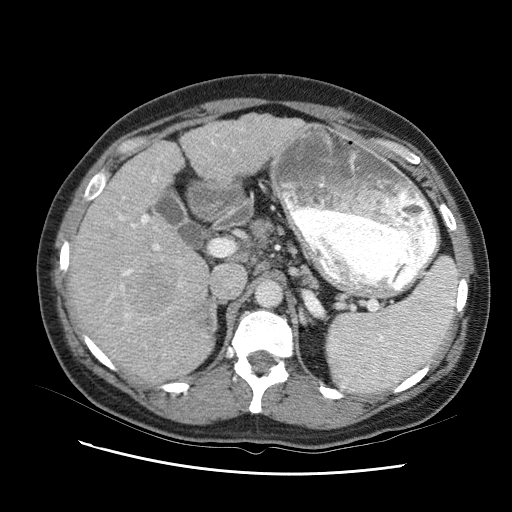
Contrast-enhanced abdominal CT (liver protocol), one axial slice. Slice 57 of 95 in the series (ordered by position). Reconstruction kernel STANDARD. 120 kVp. One of 2 acquisitions stored at this slice position. Soft-tissue window (W 400 / L 40 HU). 2.5 mm slice thickness. 512 × 512 image matrix, field of view 360 × 360 mm. From the clinical record (not read from this slice): diagnosis: hepatocellular carcinoma (patient treated with transarterial chemoembolisation; whether this scan precedes or follows treatment is not stated here); TNM stage (as recorded): Stage-I; Child-Pugh class: B; tumour differentiation: moderately differentiated; tumour nodularity: uninodular.
Outlined on this slice (semi-automatically segmented with operator editing):
- liver parenchyma outside the tumour (the mass and vessels are separate outlines, so this box may not span the whole liver): bounding box [x1, y1, x2, y2] px = [68, 108, 310, 378]
- mass: [135, 267, 174, 301]
- liver vessels: [89, 143, 237, 371]